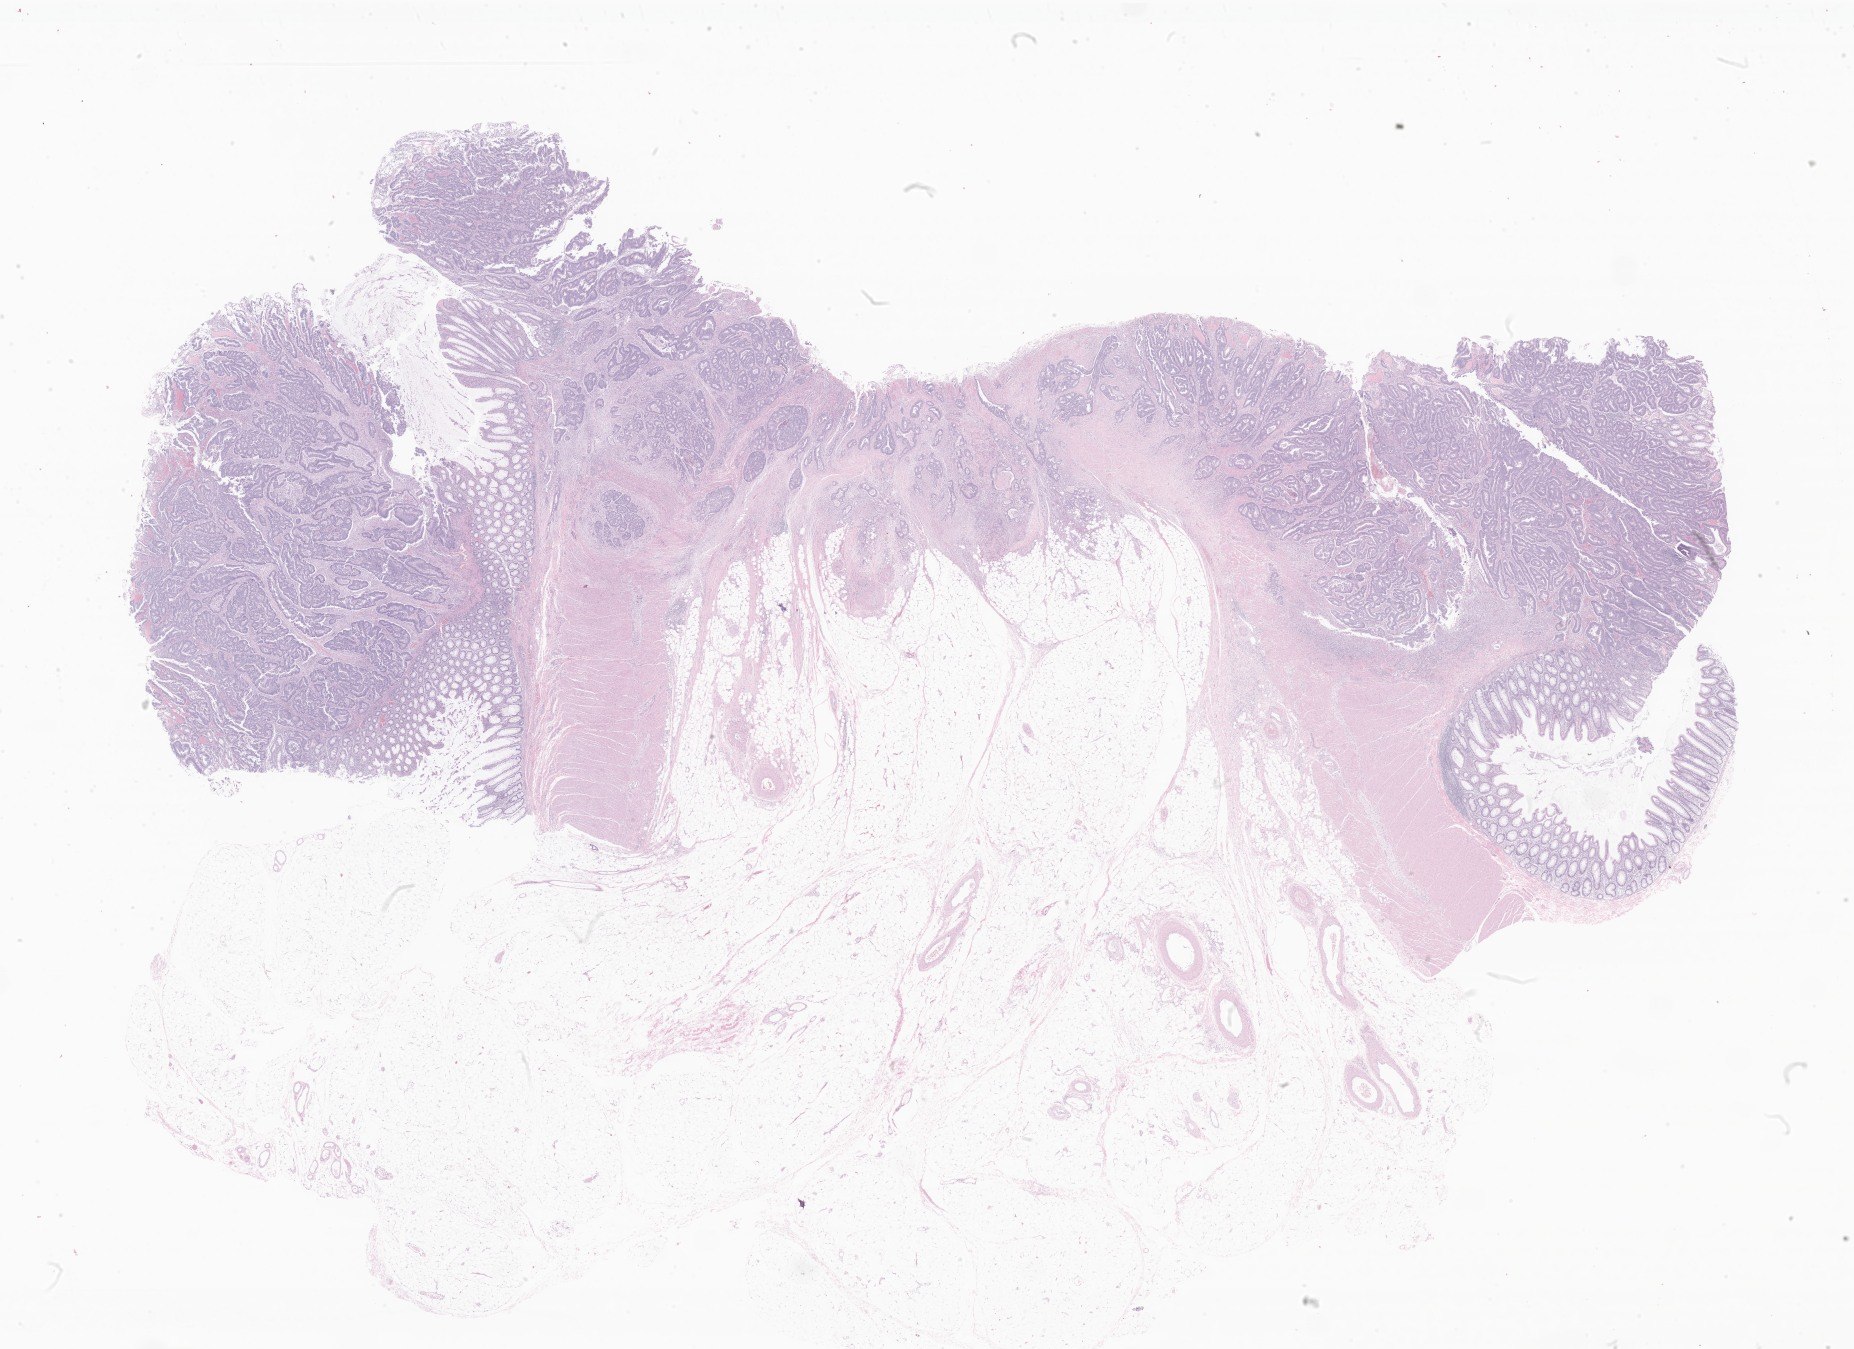
Whole-slide image, hematoxylin and eosin (H&E) stain of tumor tissue from the descending colon — shown as a low-resolution overview of the whole scanned area (about 31.3 x 22.8 mm). FFPE section. Patient female; age 193 months (16 years 1 month).
Recorded diagnosis: Adenocarcinoma, NOS.